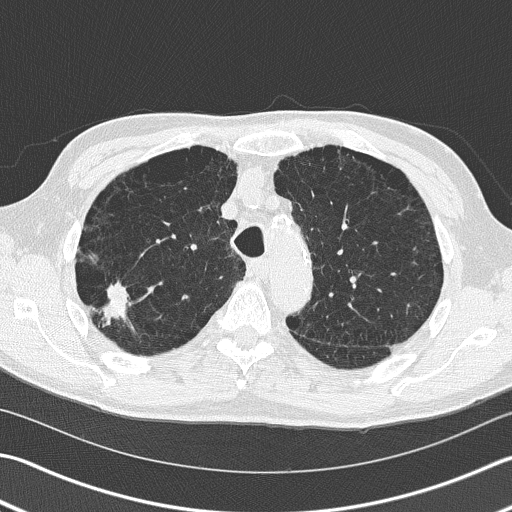
Low-dose screening chest CT, one axial slice; slice 119 of 163 in the series (ordered by position); reconstruction kernel B50f; 120 kVp; lung window (W 1500 / L -600 HU); 2 mm slice thickness; 512 × 512 image matrix, field of view 346 × 346 mm.
Outlined on this slice (manually delineated by an expert):
- lesion 1 (tumor, upper lobe of right lung): box from (x=102, y=284) to (x=130, y=324) px